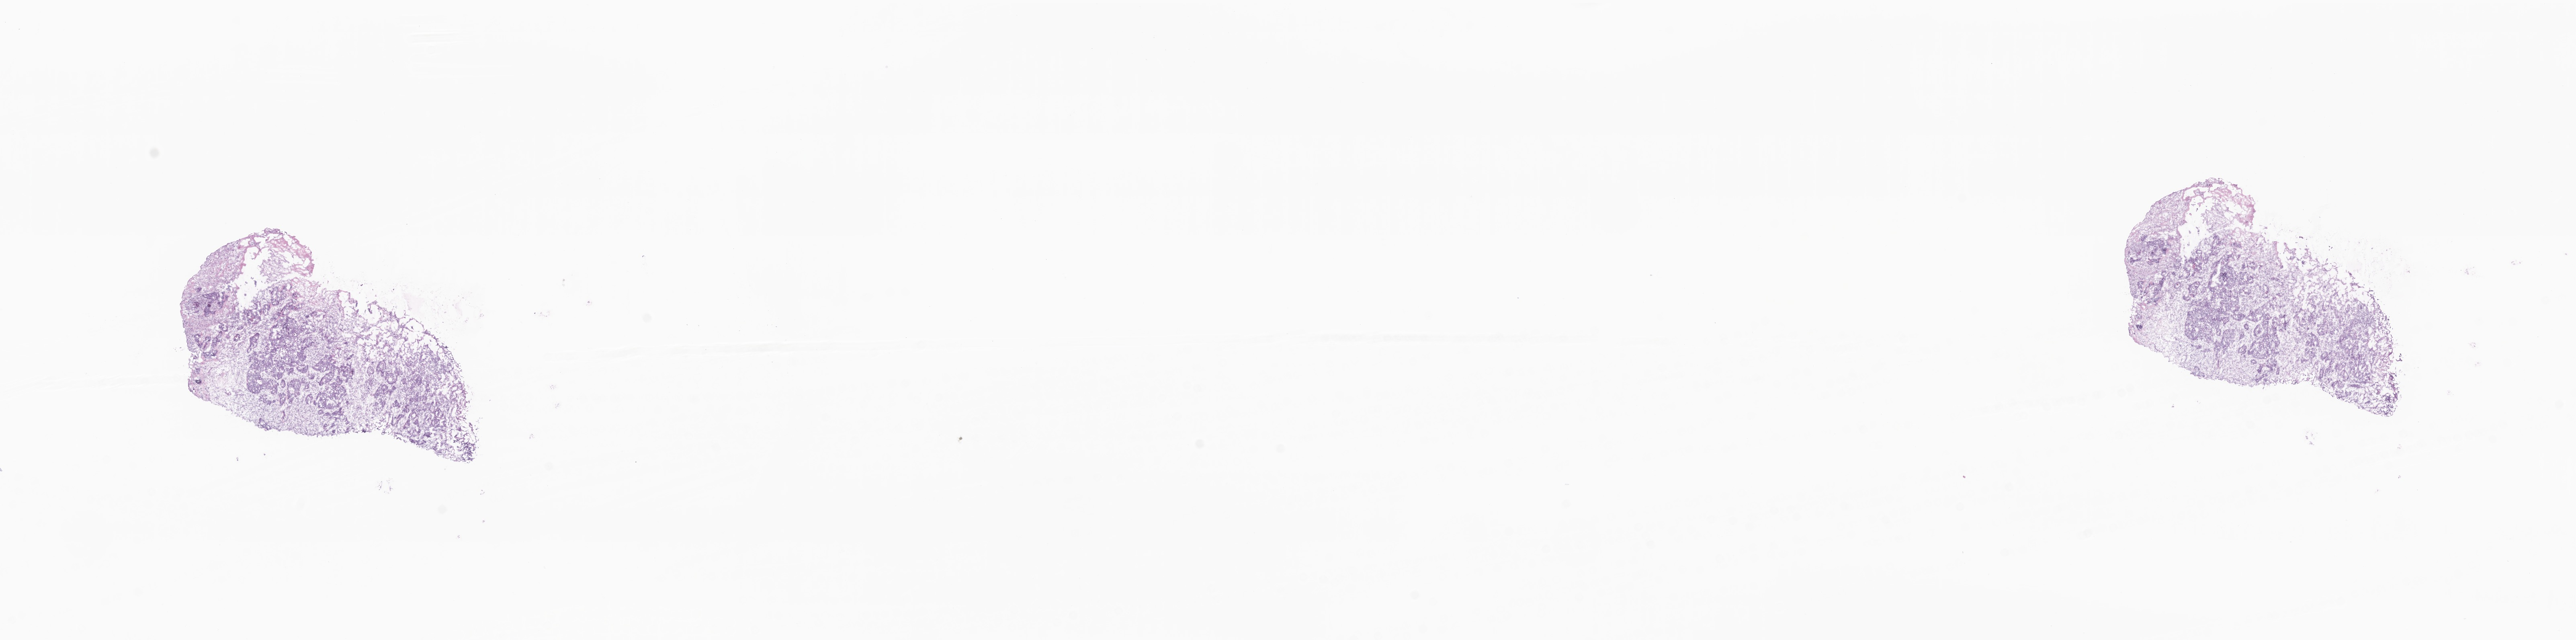
Digitized H&E-stained section — low-resolution overview of the scanned area, about 27.0 x 6.7 mm, cryosection, specimen: metastatic tumor tissue, resected from liver. Patient: male, age at initial diagnosis 53 years. Pathologist review of this section (percent, as recorded): tumor cells 40%, tumor nuclei 40%, stromal cells 45%, necrosis 0%, normal cells 15%. Inflammatory infiltration, as recorded: lymphocyte infiltration 8%, monocyte infiltration 2%, neutrophil infiltration 2%.
Section: top of the tissue portion. Patient diagnosis (primary): Adenocarcinoma, NOS.